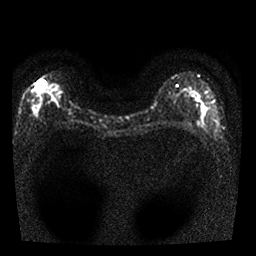
Breast MRI, one axial slice; position 14 of 25 along the scan axis; diffusion-weighted series; image 2 of 4 stored at this slice position (different b-values; order by instance number); 1.5 T; 4 mm slice thickness; 256 × 256 image matrix. Female patient.
Outlined on this slice (outlined manually by an expert reader):
- tumour on diffusion-weighted imaging: bounding box (x1, y1, x2, y2) in pixels: (35, 78, 49, 92)